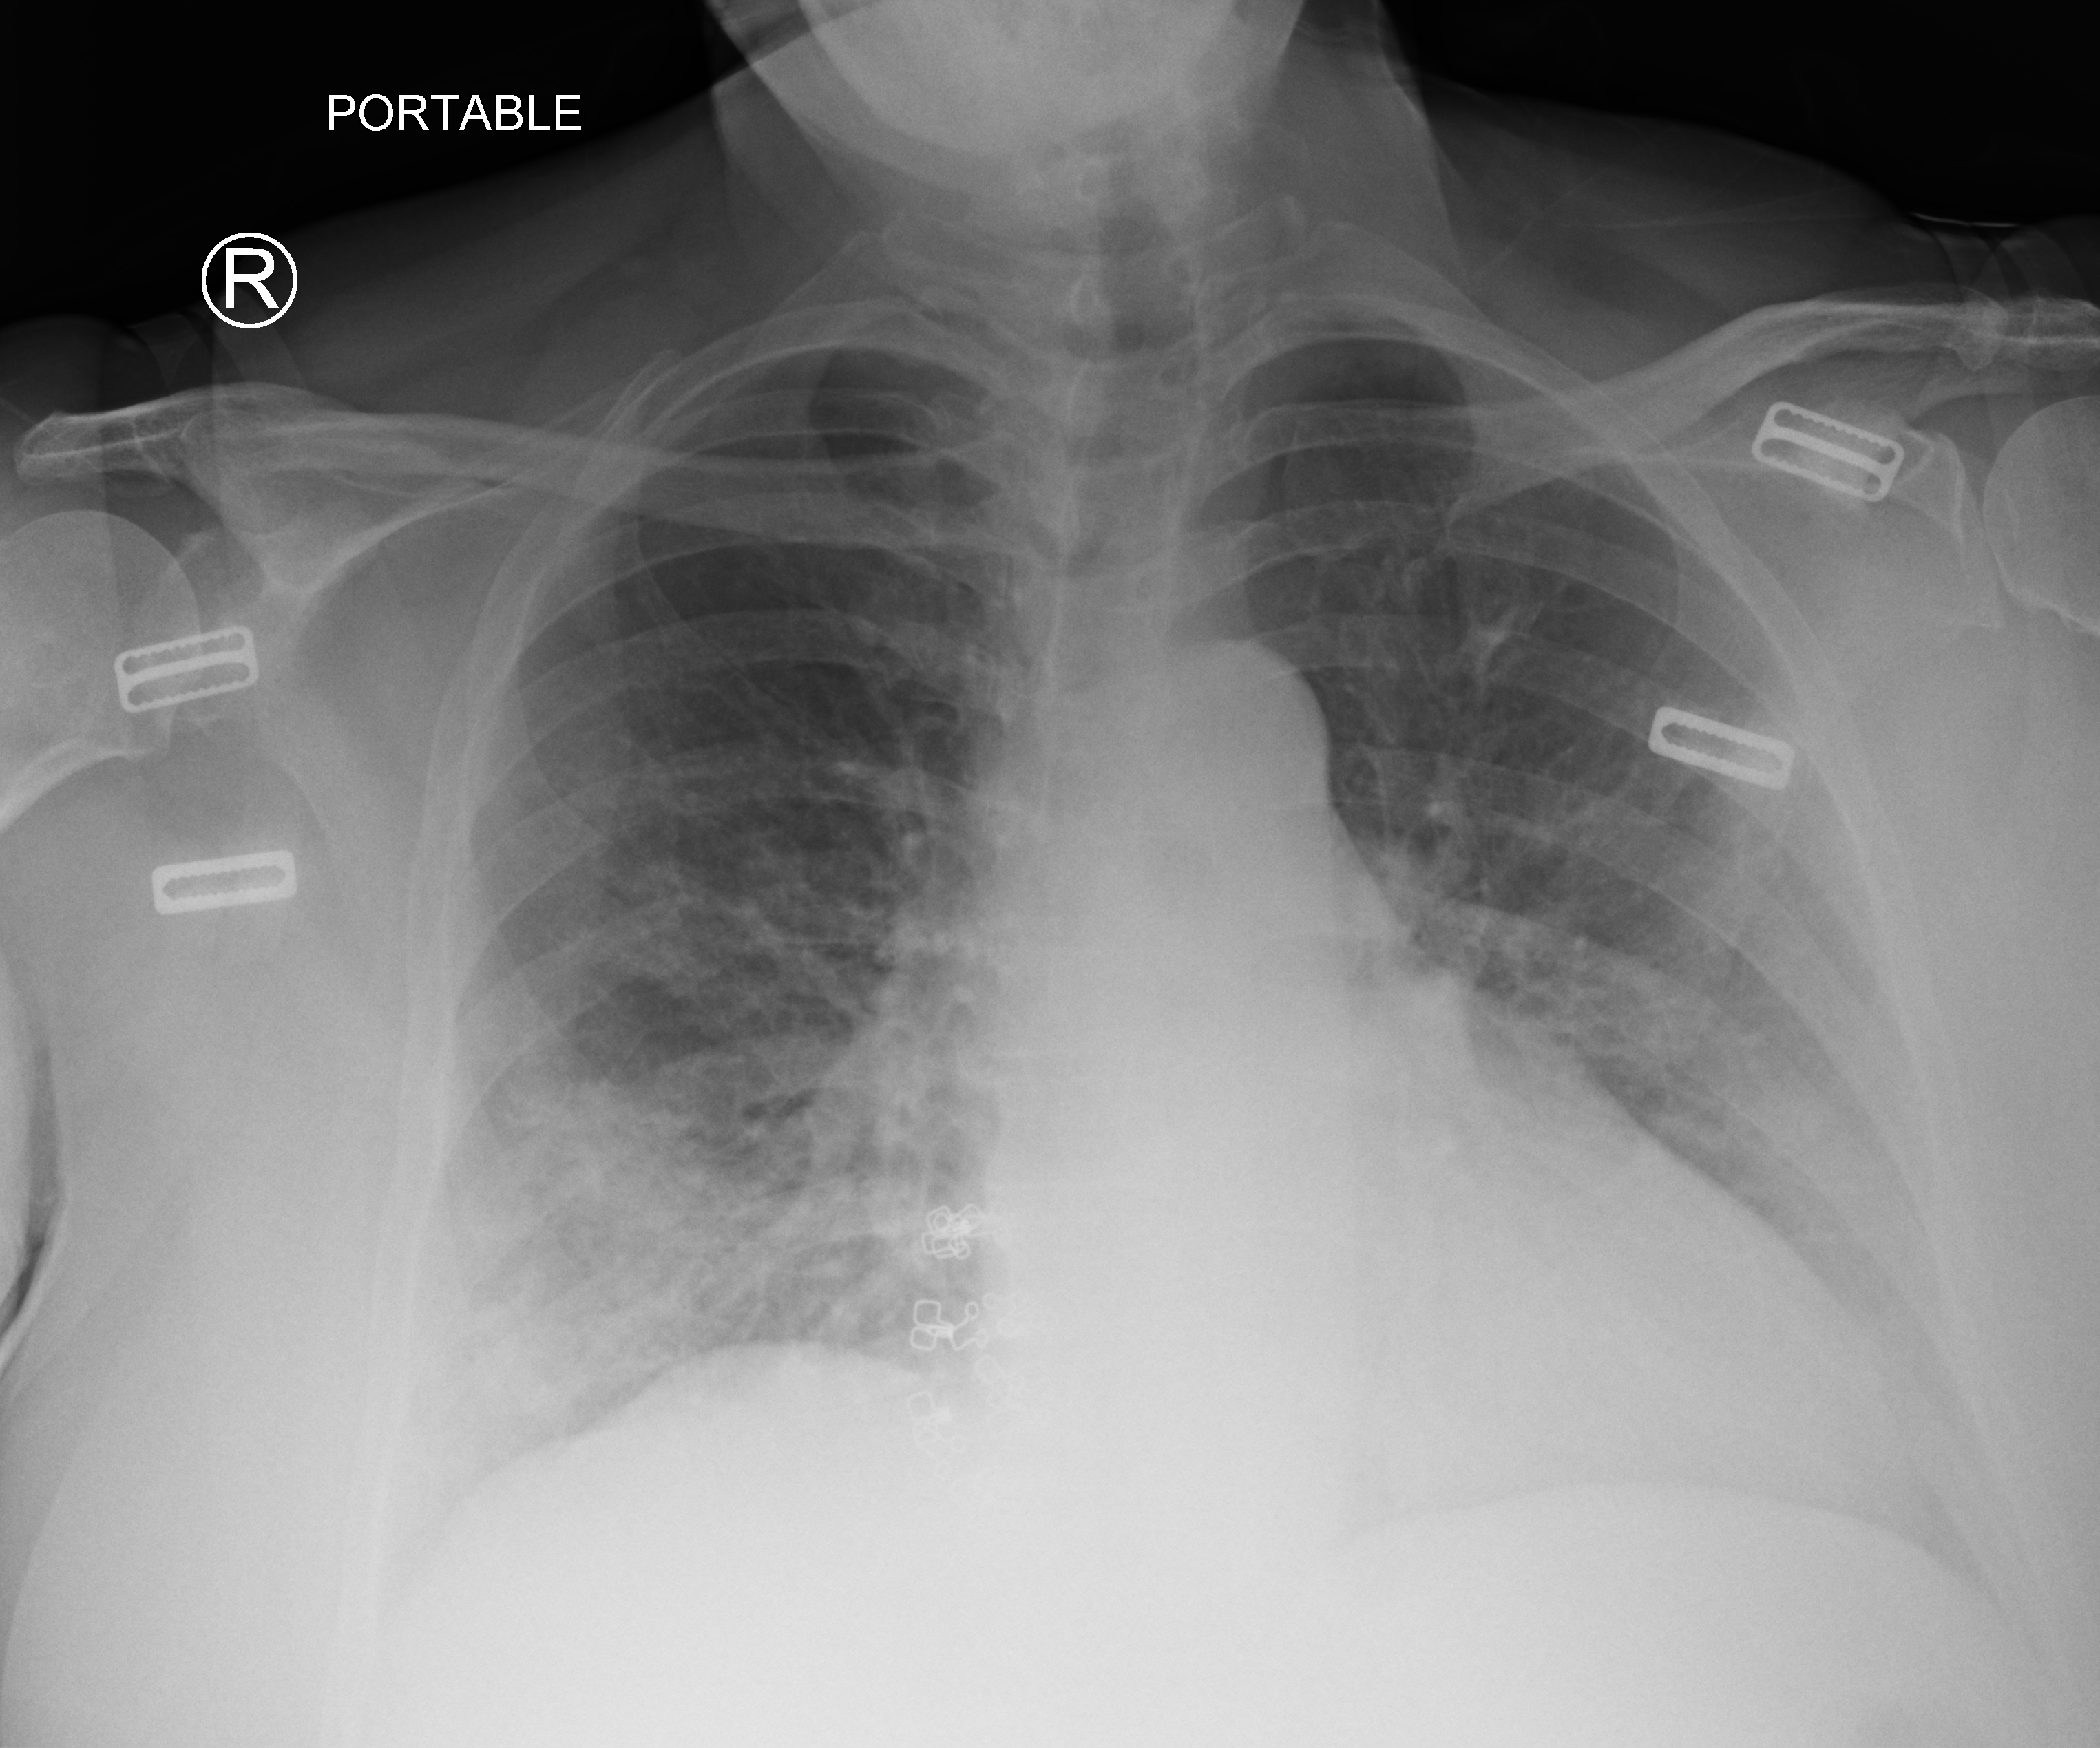
Chest X-ray (portable); anteroposterior (AP) projection. Patient hospitalised with COVID-19; female, aged 60–74 years.
Hospital-stay facts (about this admission, not read from this image; timing relative to this image not recorded): mechanically ventilated during this hospital stay: no; smoking status (admission record): former; admitted to intensive care during this hospital stay: no.